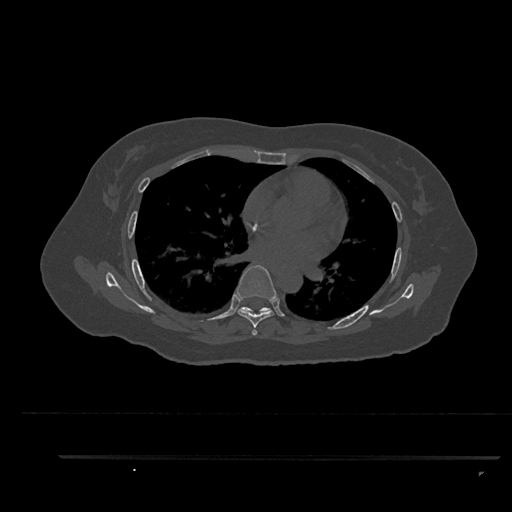
CT including the spine, one axial slice; slice 545 of 797 in the series (ordered by position); bone window (W 1800 / L 400 HU); 0.5 mm slice thickness; 512 × 512 image matrix, field of view 408 × 408 mm. Patient: female, 44 years. From the clinical record (not read from this slice): primary cancer: renal; vertebrae with lytic lesions (as recorded): L1.
Structures marked on this image (semi-automatic segmentation, software-assisted and operator-edited):
- T6 vertebra: box from (x=235, y=265) to (x=276, y=335) px
- T7 vertebra: (x=242, y=307)–(x=272, y=314)